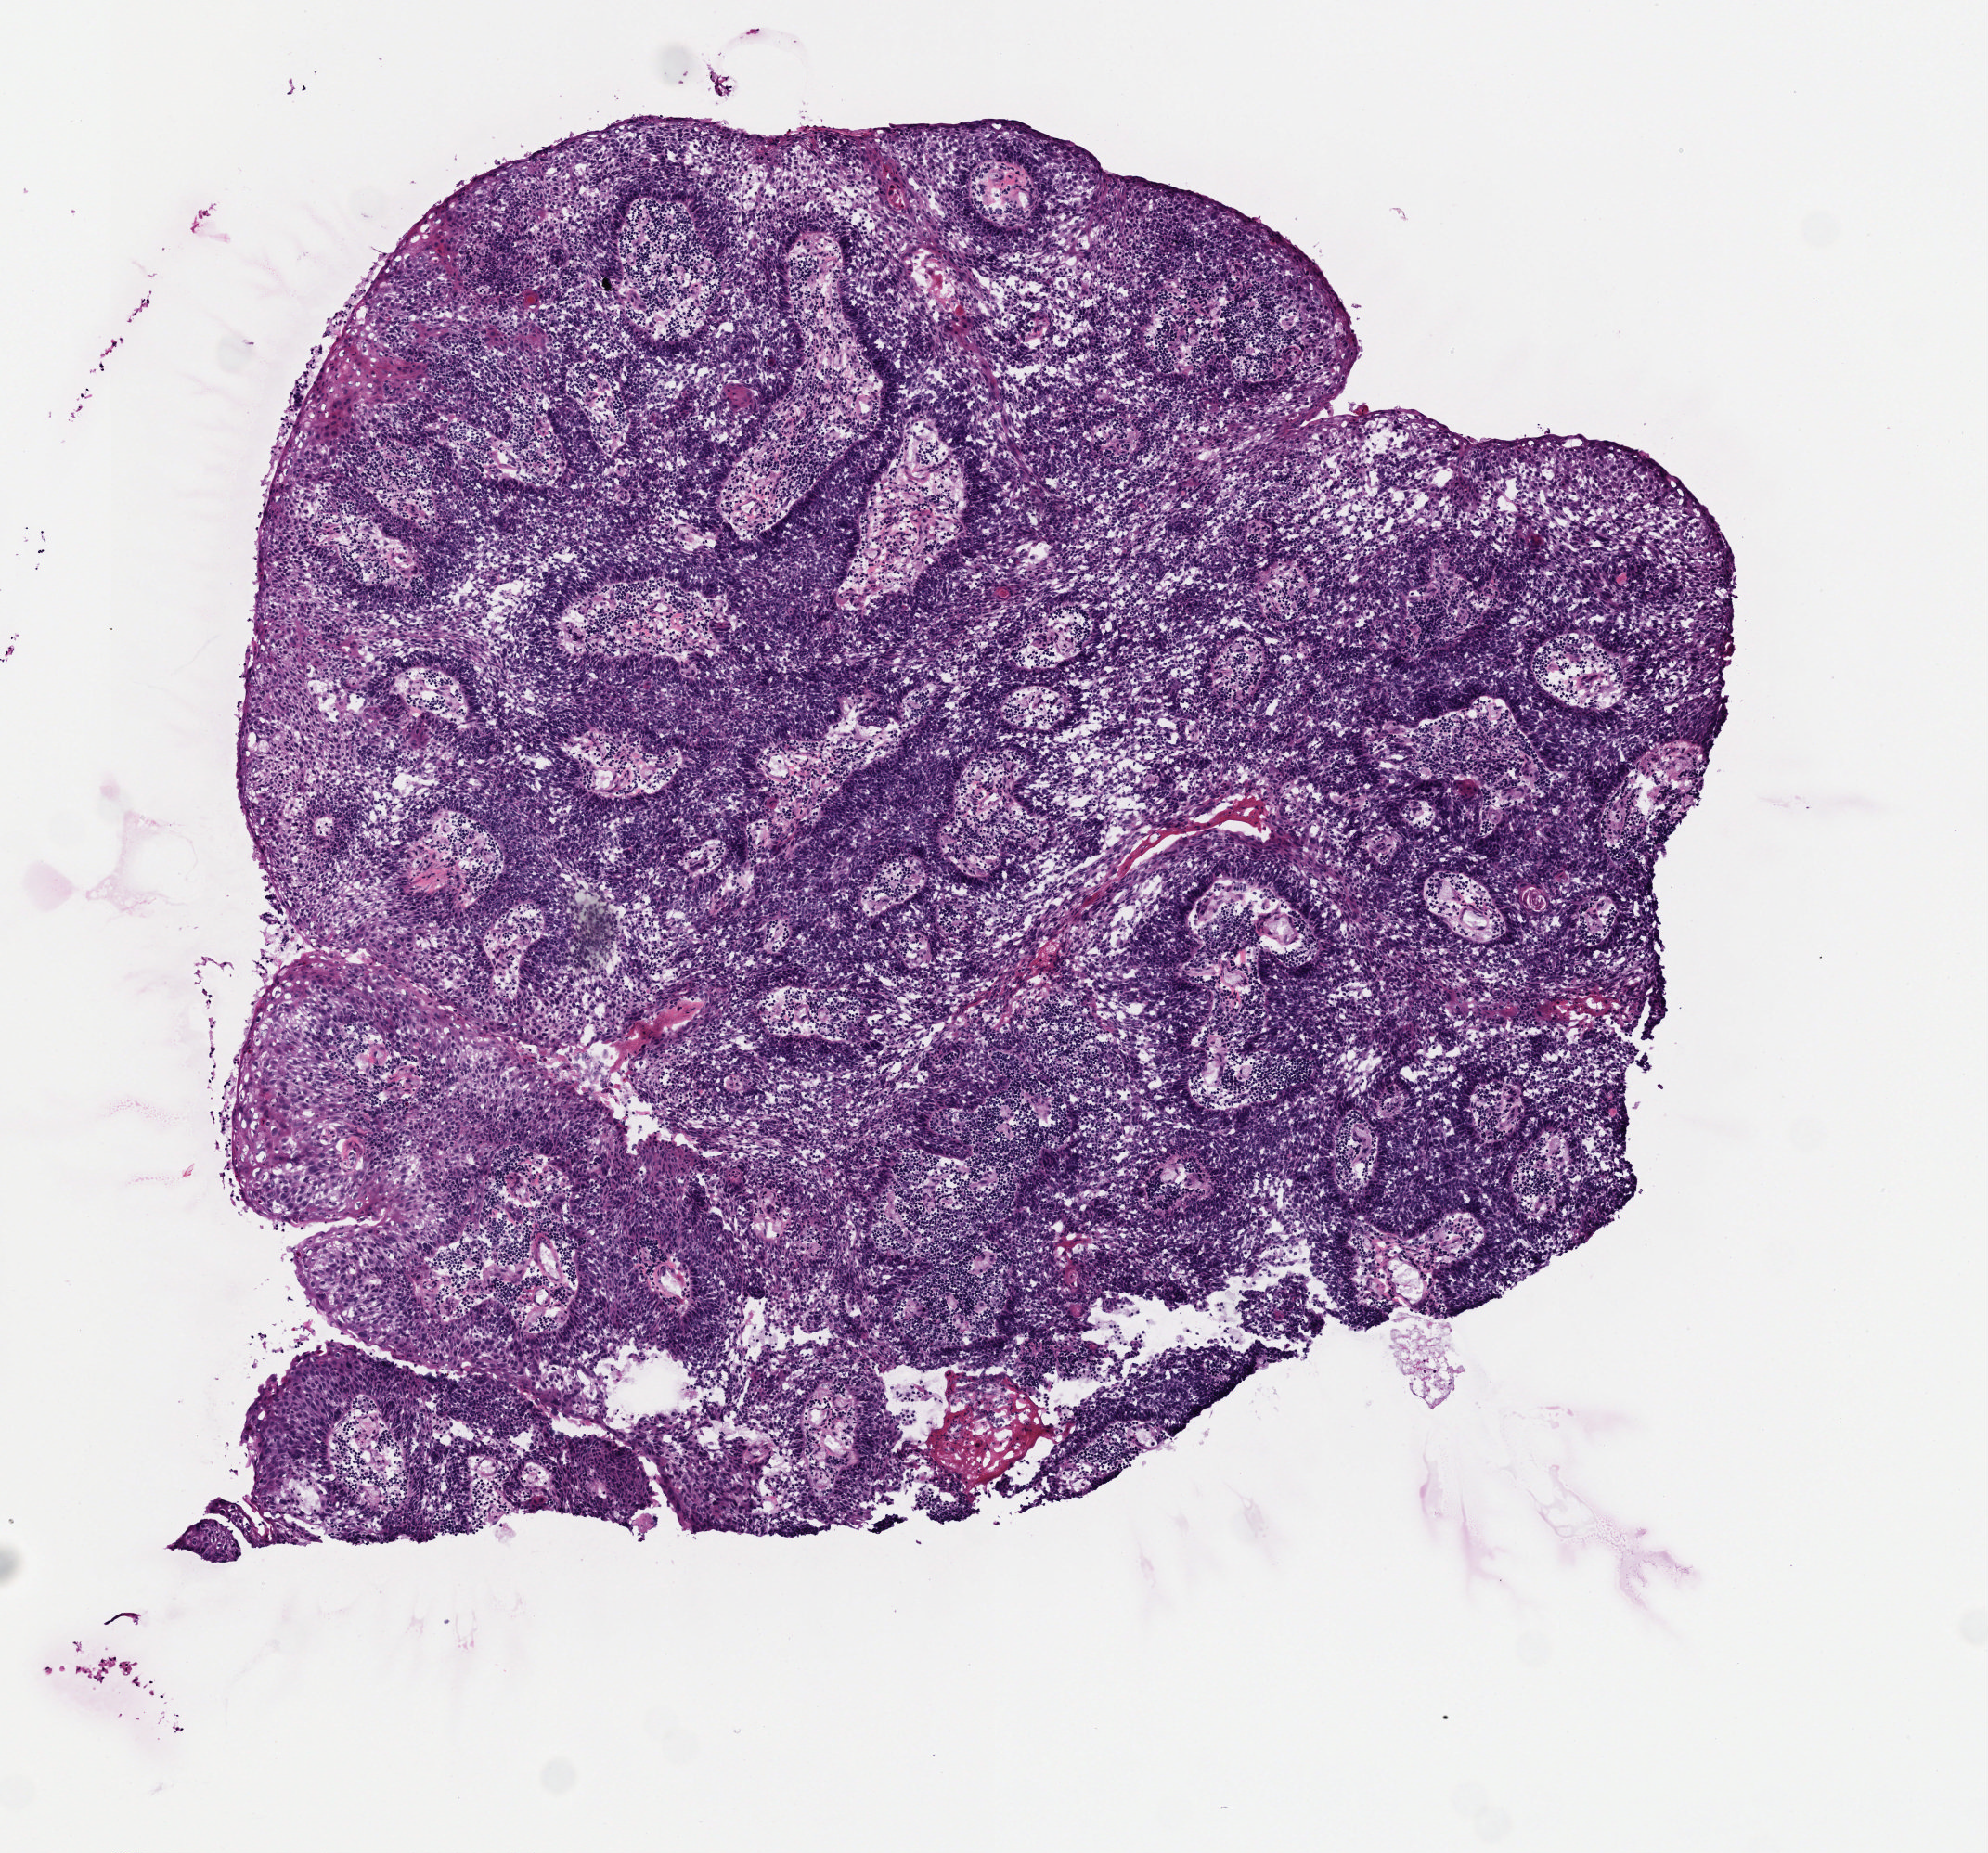
Digitized H&E-stained tissue section (whole slide) — a low-resolution overview of the entire scanned area, about 4.2 x 3.9 mm (slide scanned at 40x); frozen section; sample: primary tumour, head and neck. Patient: male, age at initial diagnosis 49 years. Slide review estimates, as recorded: tumour cells 80%, tumour nuclei 75%.
Histologic diagnosis: Basaloid squamous cell carcinoma (base of tongue, NOS).